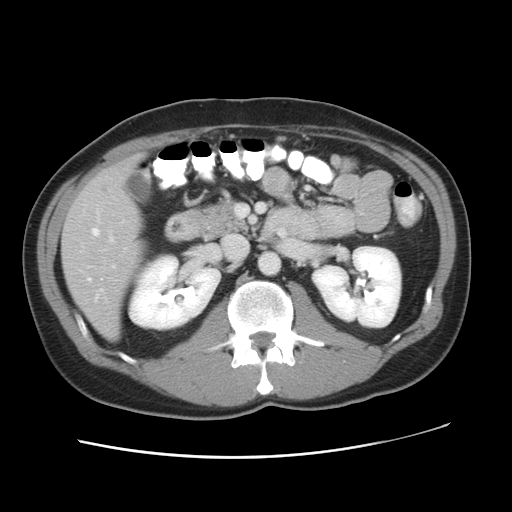
Contrast-enhanced abdominal CT, one axial slice. Slice 22 of 49 in the series (ordered by position). Reconstruction kernel STANDARD. 120 kVp. Intravenous contrast given. Soft-tissue window (W 400 / L 40 HU). 5 mm slice thickness. 512 × 512 image matrix, field of view 363 × 363 mm. Male patient, age 41 years. From the clinical record (not read from this slice): diagnosis: colorectal cancer liver metastases, imaged before liver resection.
Outlined on this slice (outlined manually by an expert reader):
- hepatic veins: bounding box [x1, y1, x2, y2] px = [88, 228, 102, 299]
- liver: [63, 156, 141, 338]
- planned liver remnant (the part of the liver to remain after resection): [115, 156, 140, 176]
- portal vein (with intrahepatic branches): [110, 236, 113, 241]
- liver metastasis: [100, 185, 112, 196]